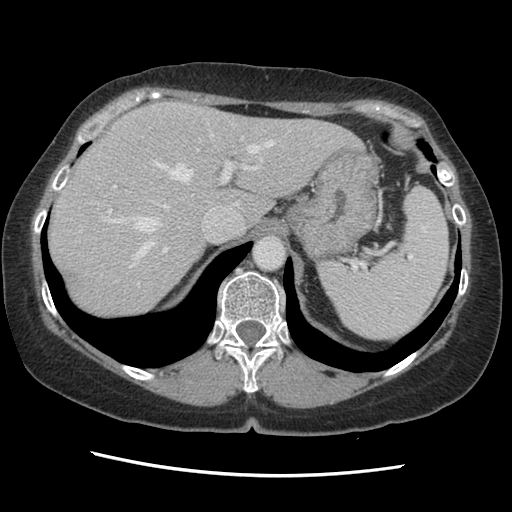
Contrast-enhanced abdominal CT, one axial slice. Position 103 of 141 along the scan axis. Soft-tissue window (W 400 / L 40 HU). 512 × 512 image matrix, field of view 330 × 330 mm. Female patient, age 61 years. Case-level facts recorded for this patient, not image findings: diagnosis: colorectal cancer liver metastases, imaged before liver resection; multiple liver metastases: no.
Annotated regions visible in this slice (expert manual segmentation):
- hepatic veins: box from (x=97, y=122) to (x=274, y=286) px
- liver: (x=49, y=103)–(x=359, y=319)
- planned liver remnant (the part of the liver to remain after resection): (x=48, y=103)–(x=358, y=319)
- portal vein (with intrahepatic branches): (x=108, y=137)–(x=259, y=252)